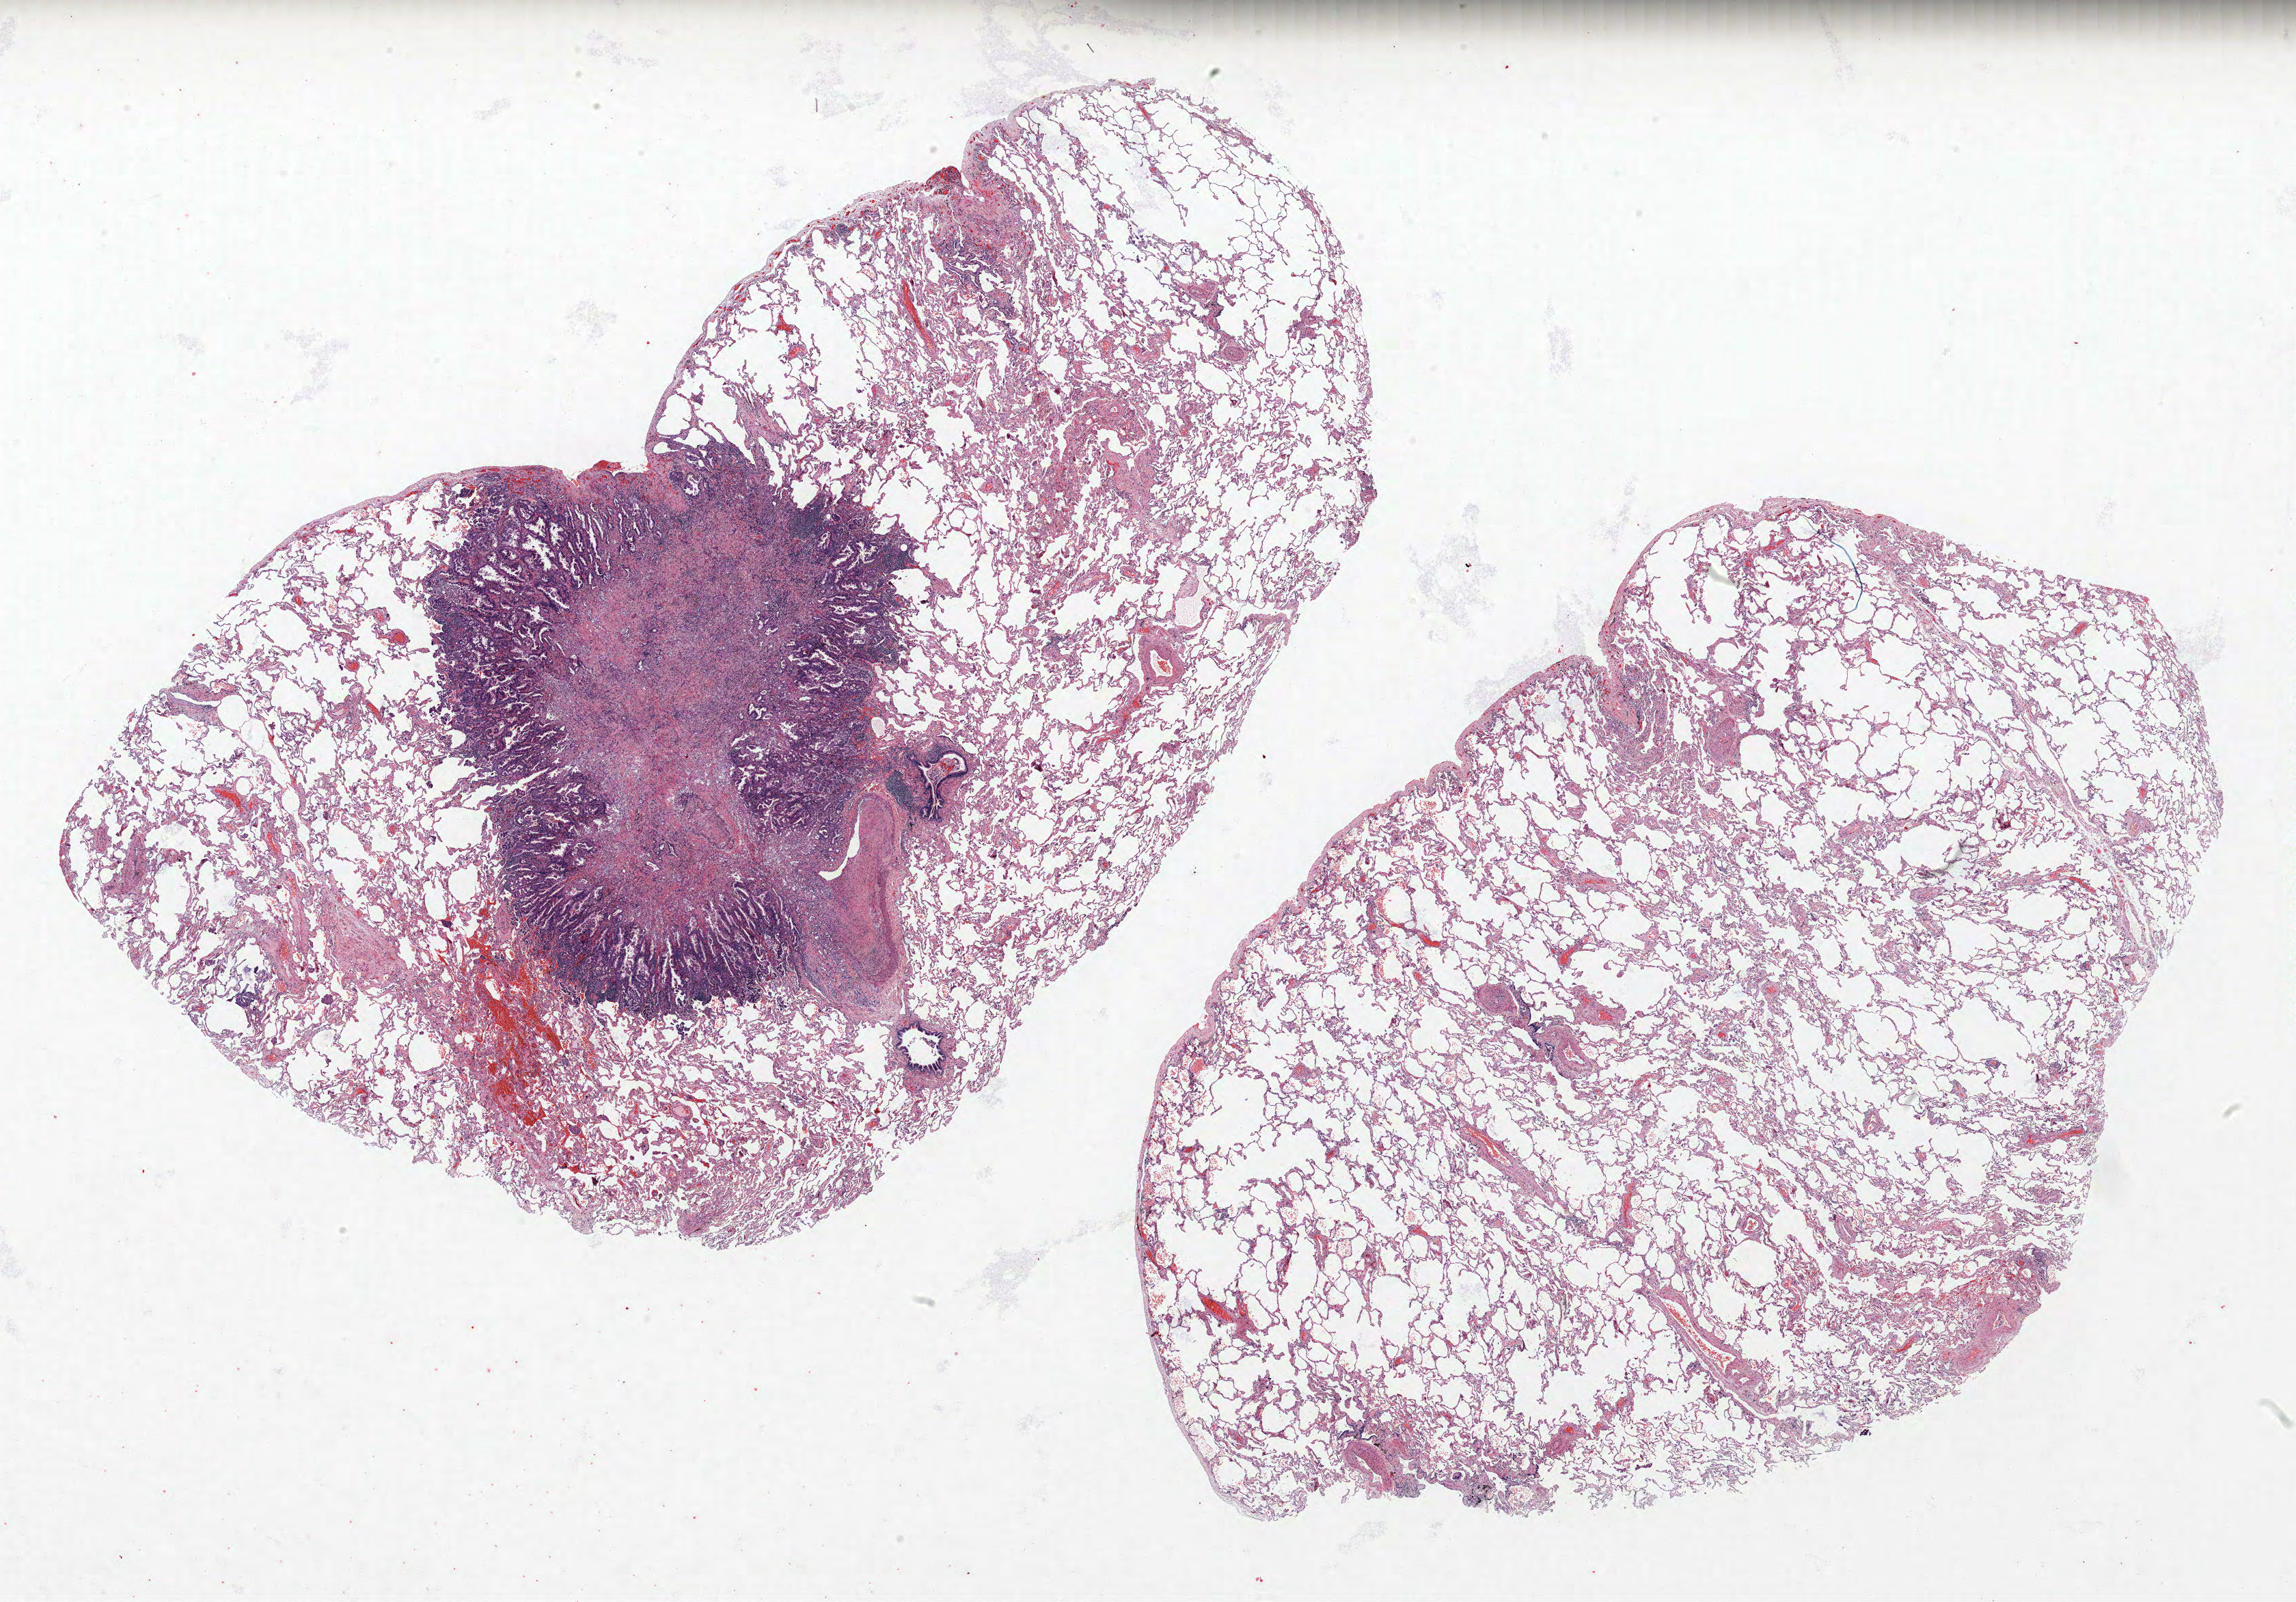
H&E whole-slide image, shown as a low-resolution overview of the whole scanned area (about 26.9 x 18.8 mm, acquisition: 40x scan); FFPE section; lung. Male, age 62 at enrolment. Grade: moderately differentiated (G2).
Primary tumour location (clinical record): right upper lobe. Tumour size (pathology): 7 mm. Participant's lung-cancer diagnosis: Adenocarcinoma, NOS. ICD-O-3 topography: upper lobe of lung (C34.1). Stage (AJCC 6th edition): IA.